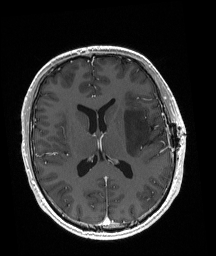
Brain MRI from a brain-tumour surgery series, one axial slice. Position 89 of 192 along the scan axis. T1-weighted post-contrast. 1 mm slice thickness. 216 × 256 image matrix, field of view 211 × 250 mm. Case-level facts recorded for this patient, not image findings: histopathology: Astrocytoma; WHO grade: 3; IDH mutation: yes.
Annotated regions visible in this slice (expert manual segmentation):
- tumour: bounding box (x1, y1, x2, y2) in pixels: (124, 109, 162, 157)